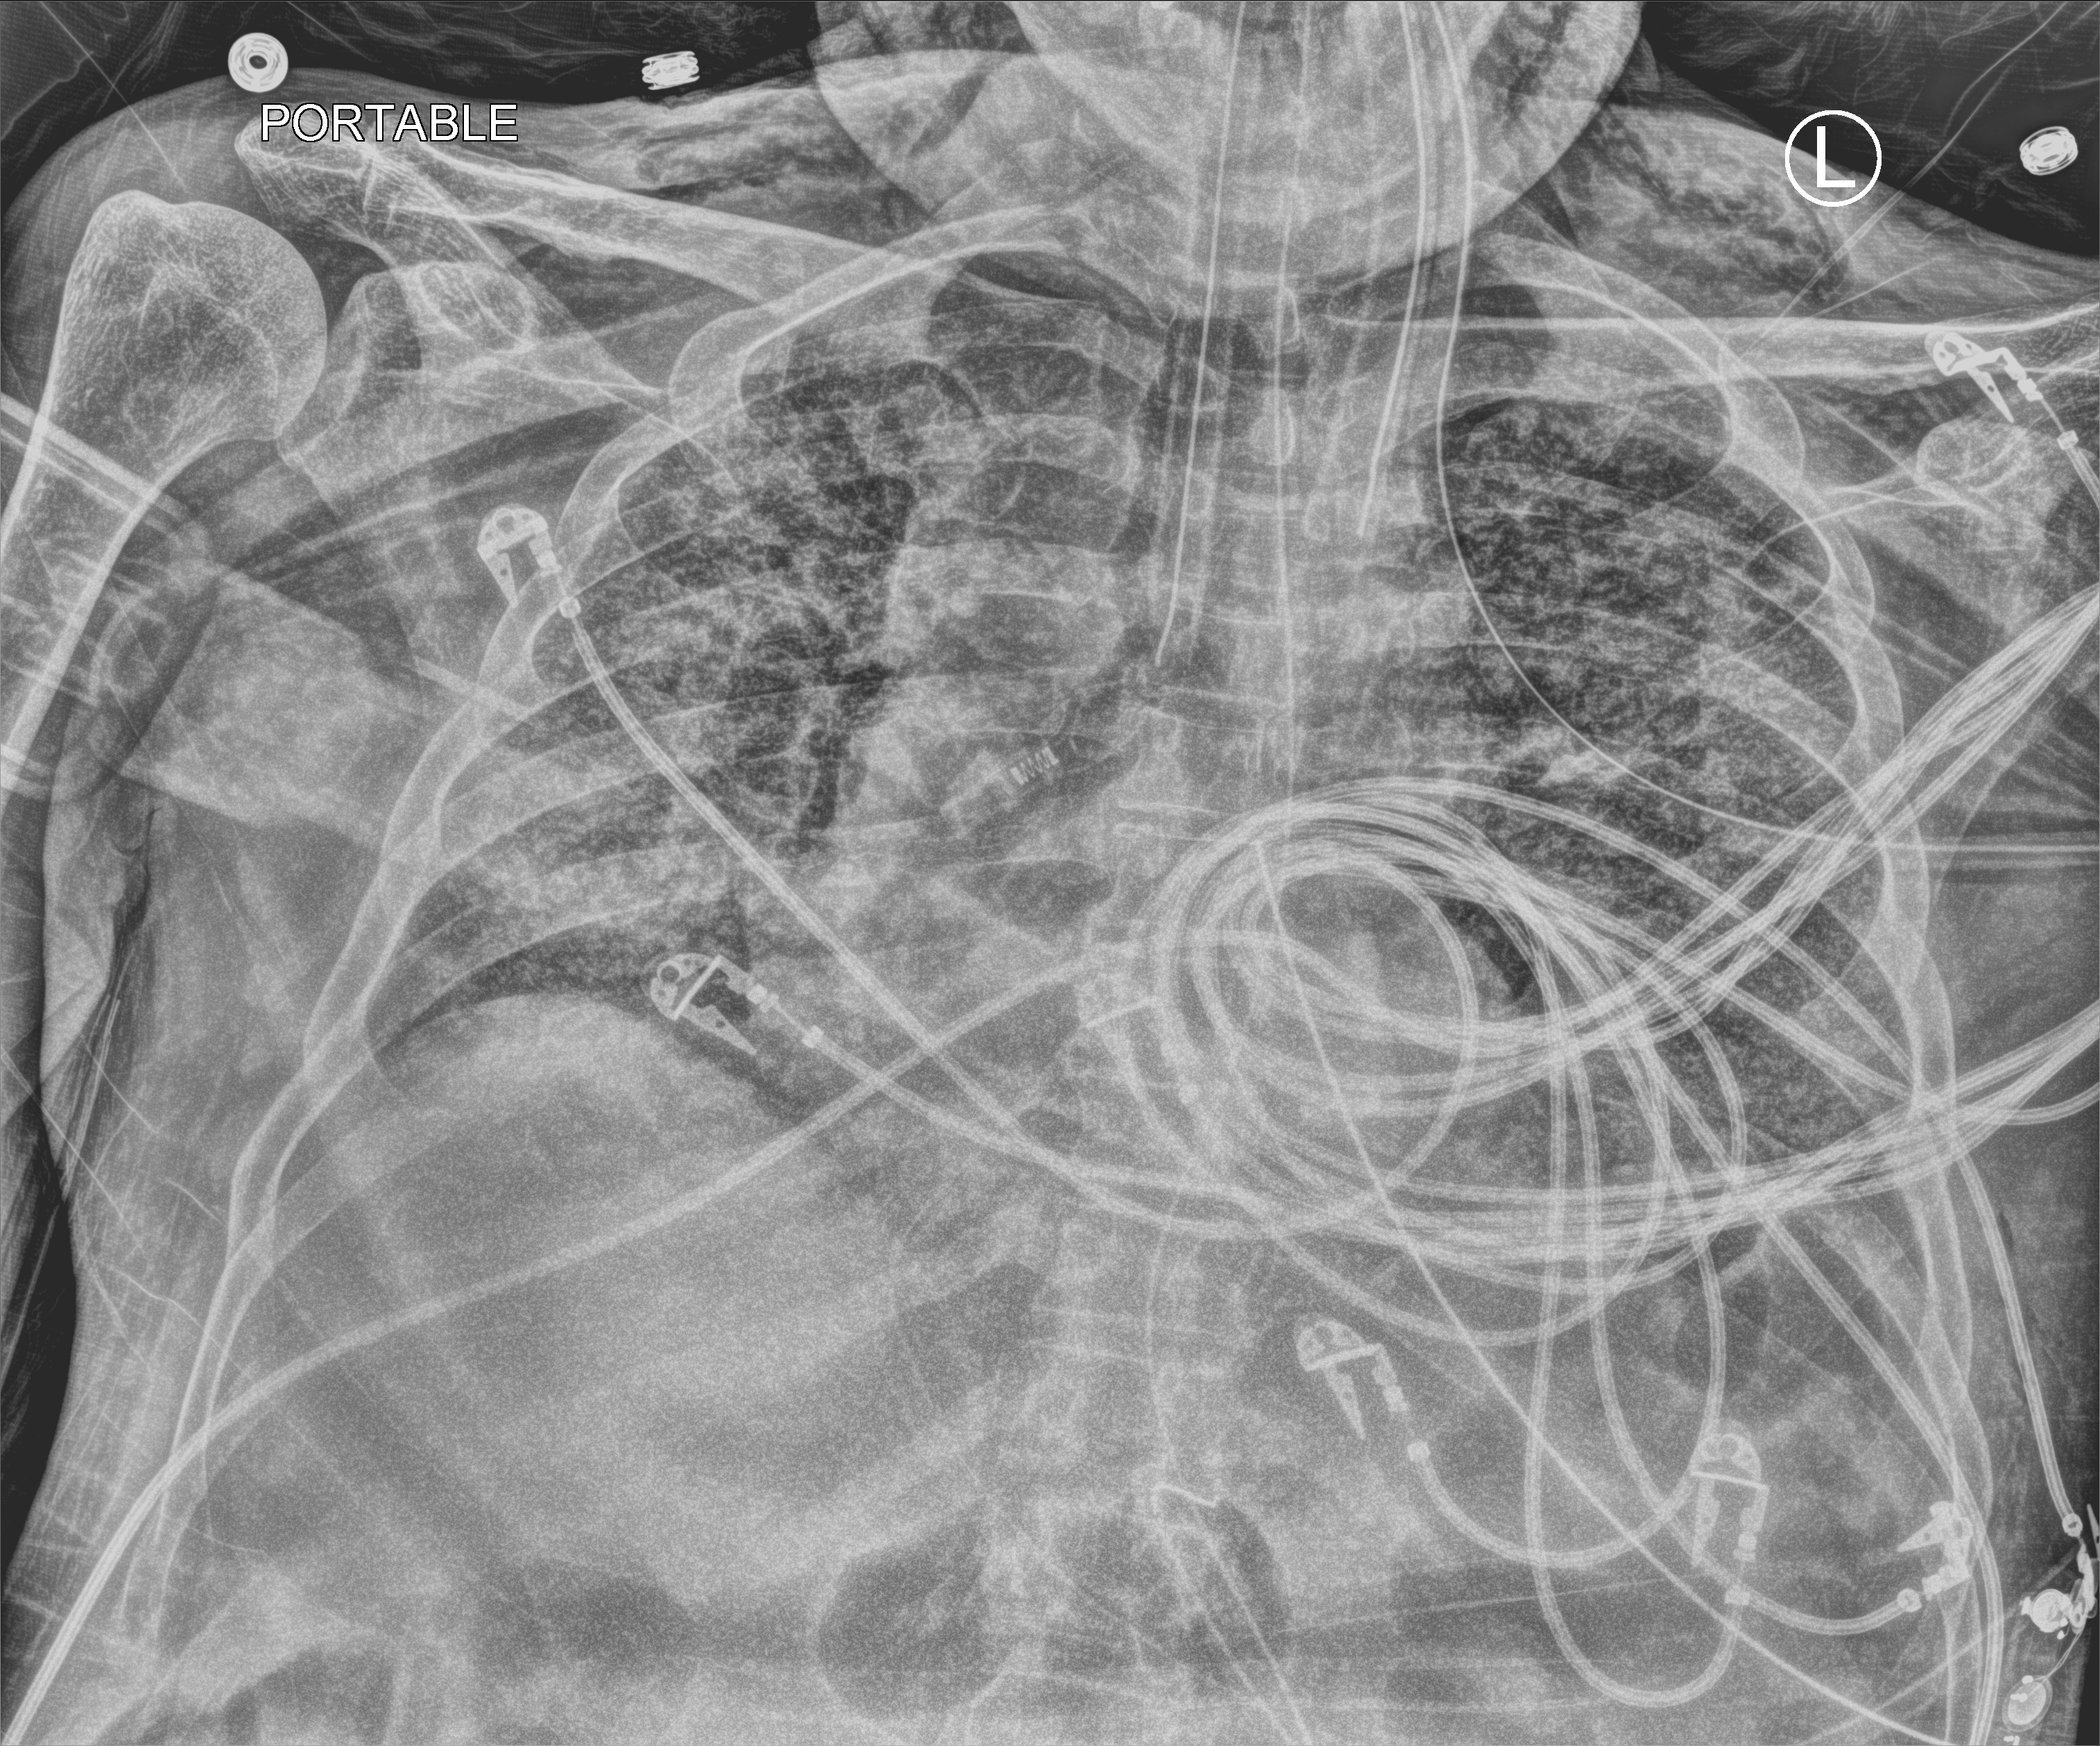
Portable chest radiograph; anteroposterior (AP) projection. Patient hospitalised with COVID-19; male, aged 60–74 years.
Hospital-stay facts (about this admission, not read from this image; timing relative to this image not recorded): admitted to intensive care during this hospital stay: yes; mechanically ventilated during this hospital stay: yes.